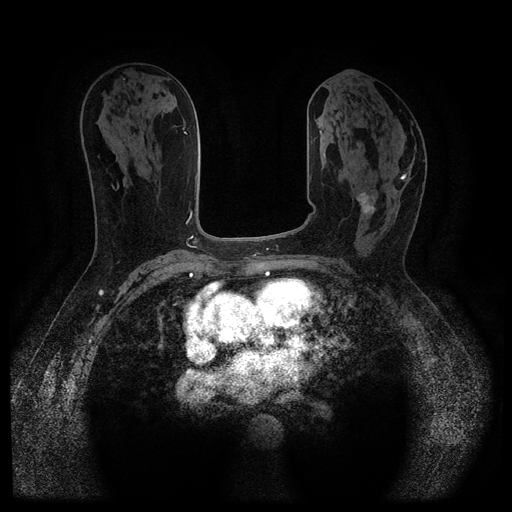
Breast MRI (dynamic contrast-enhanced, multi-phase), one axial slice; slice 53 of 116 in the series (ordered by position); dynamic contrast-enhanced series, time point 2 of 5 at this slice position (early post-contrast); 1.5 T; TE 2.6 ms, TR 5.4 ms; 2 mm slice thickness; 512 × 512 image matrix, field of view 340 × 340 mm. Female patient, age 64 years.
Outlined on this slice (semi-automatically segmented with operator editing):
- breast lesion (labelled 'tumour' in the annotation; benign lesions carry a separate 'benign' label): box from (x=356, y=192) to (x=377, y=215) px